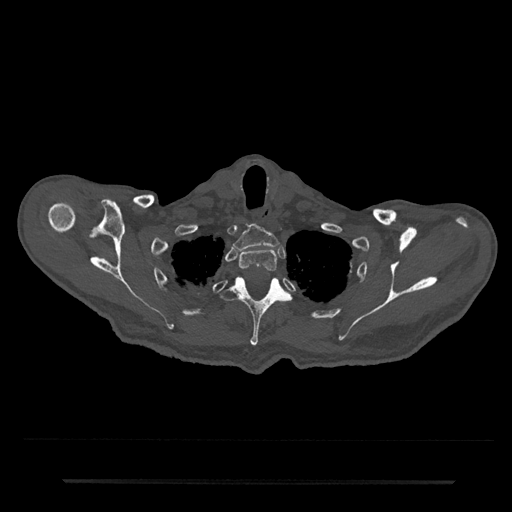
CT including the spine, one axial slice. Position 677 of 797 along the scan axis. Bone window (W 1800 / L 400 HU). 512 × 512 image matrix, field of view 427 × 427 mm. Patient: male, 74 years. From the clinical record (not read from this slice): primary cancer: prostate.
Structures marked on this image (semi-automatically segmented with operator editing):
- T1 vertebra: bounding box [x1, y1, x2, y2] px = [233, 225, 279, 251]
- T2 vertebra: [239, 248, 278, 273]
- T3 vertebra: [220, 277, 291, 346]